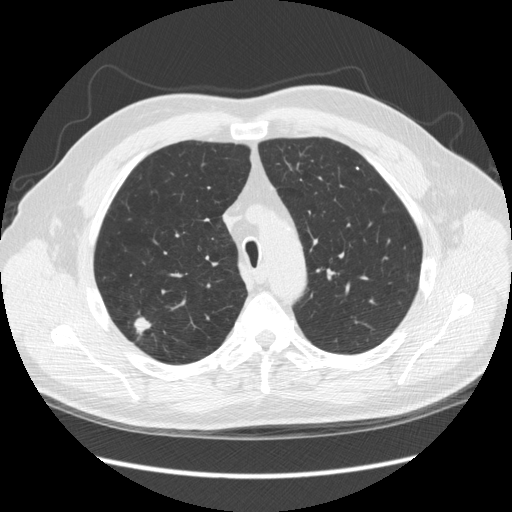
Low-dose screening chest CT, one axial slice; slice 188 of 248 in the series (ordered by position); 120 kVp; lung window (W 1500 / L -600 HU); 2.5 mm slice thickness; 512 × 512 image matrix, field of view 380 × 380 mm.
Structures marked on this image (manually delineated by an expert):
- lesion 1 (tumor, upper lobe of right lung): bounding box [x1, y1, x2, y2] px = [134, 317, 152, 334]